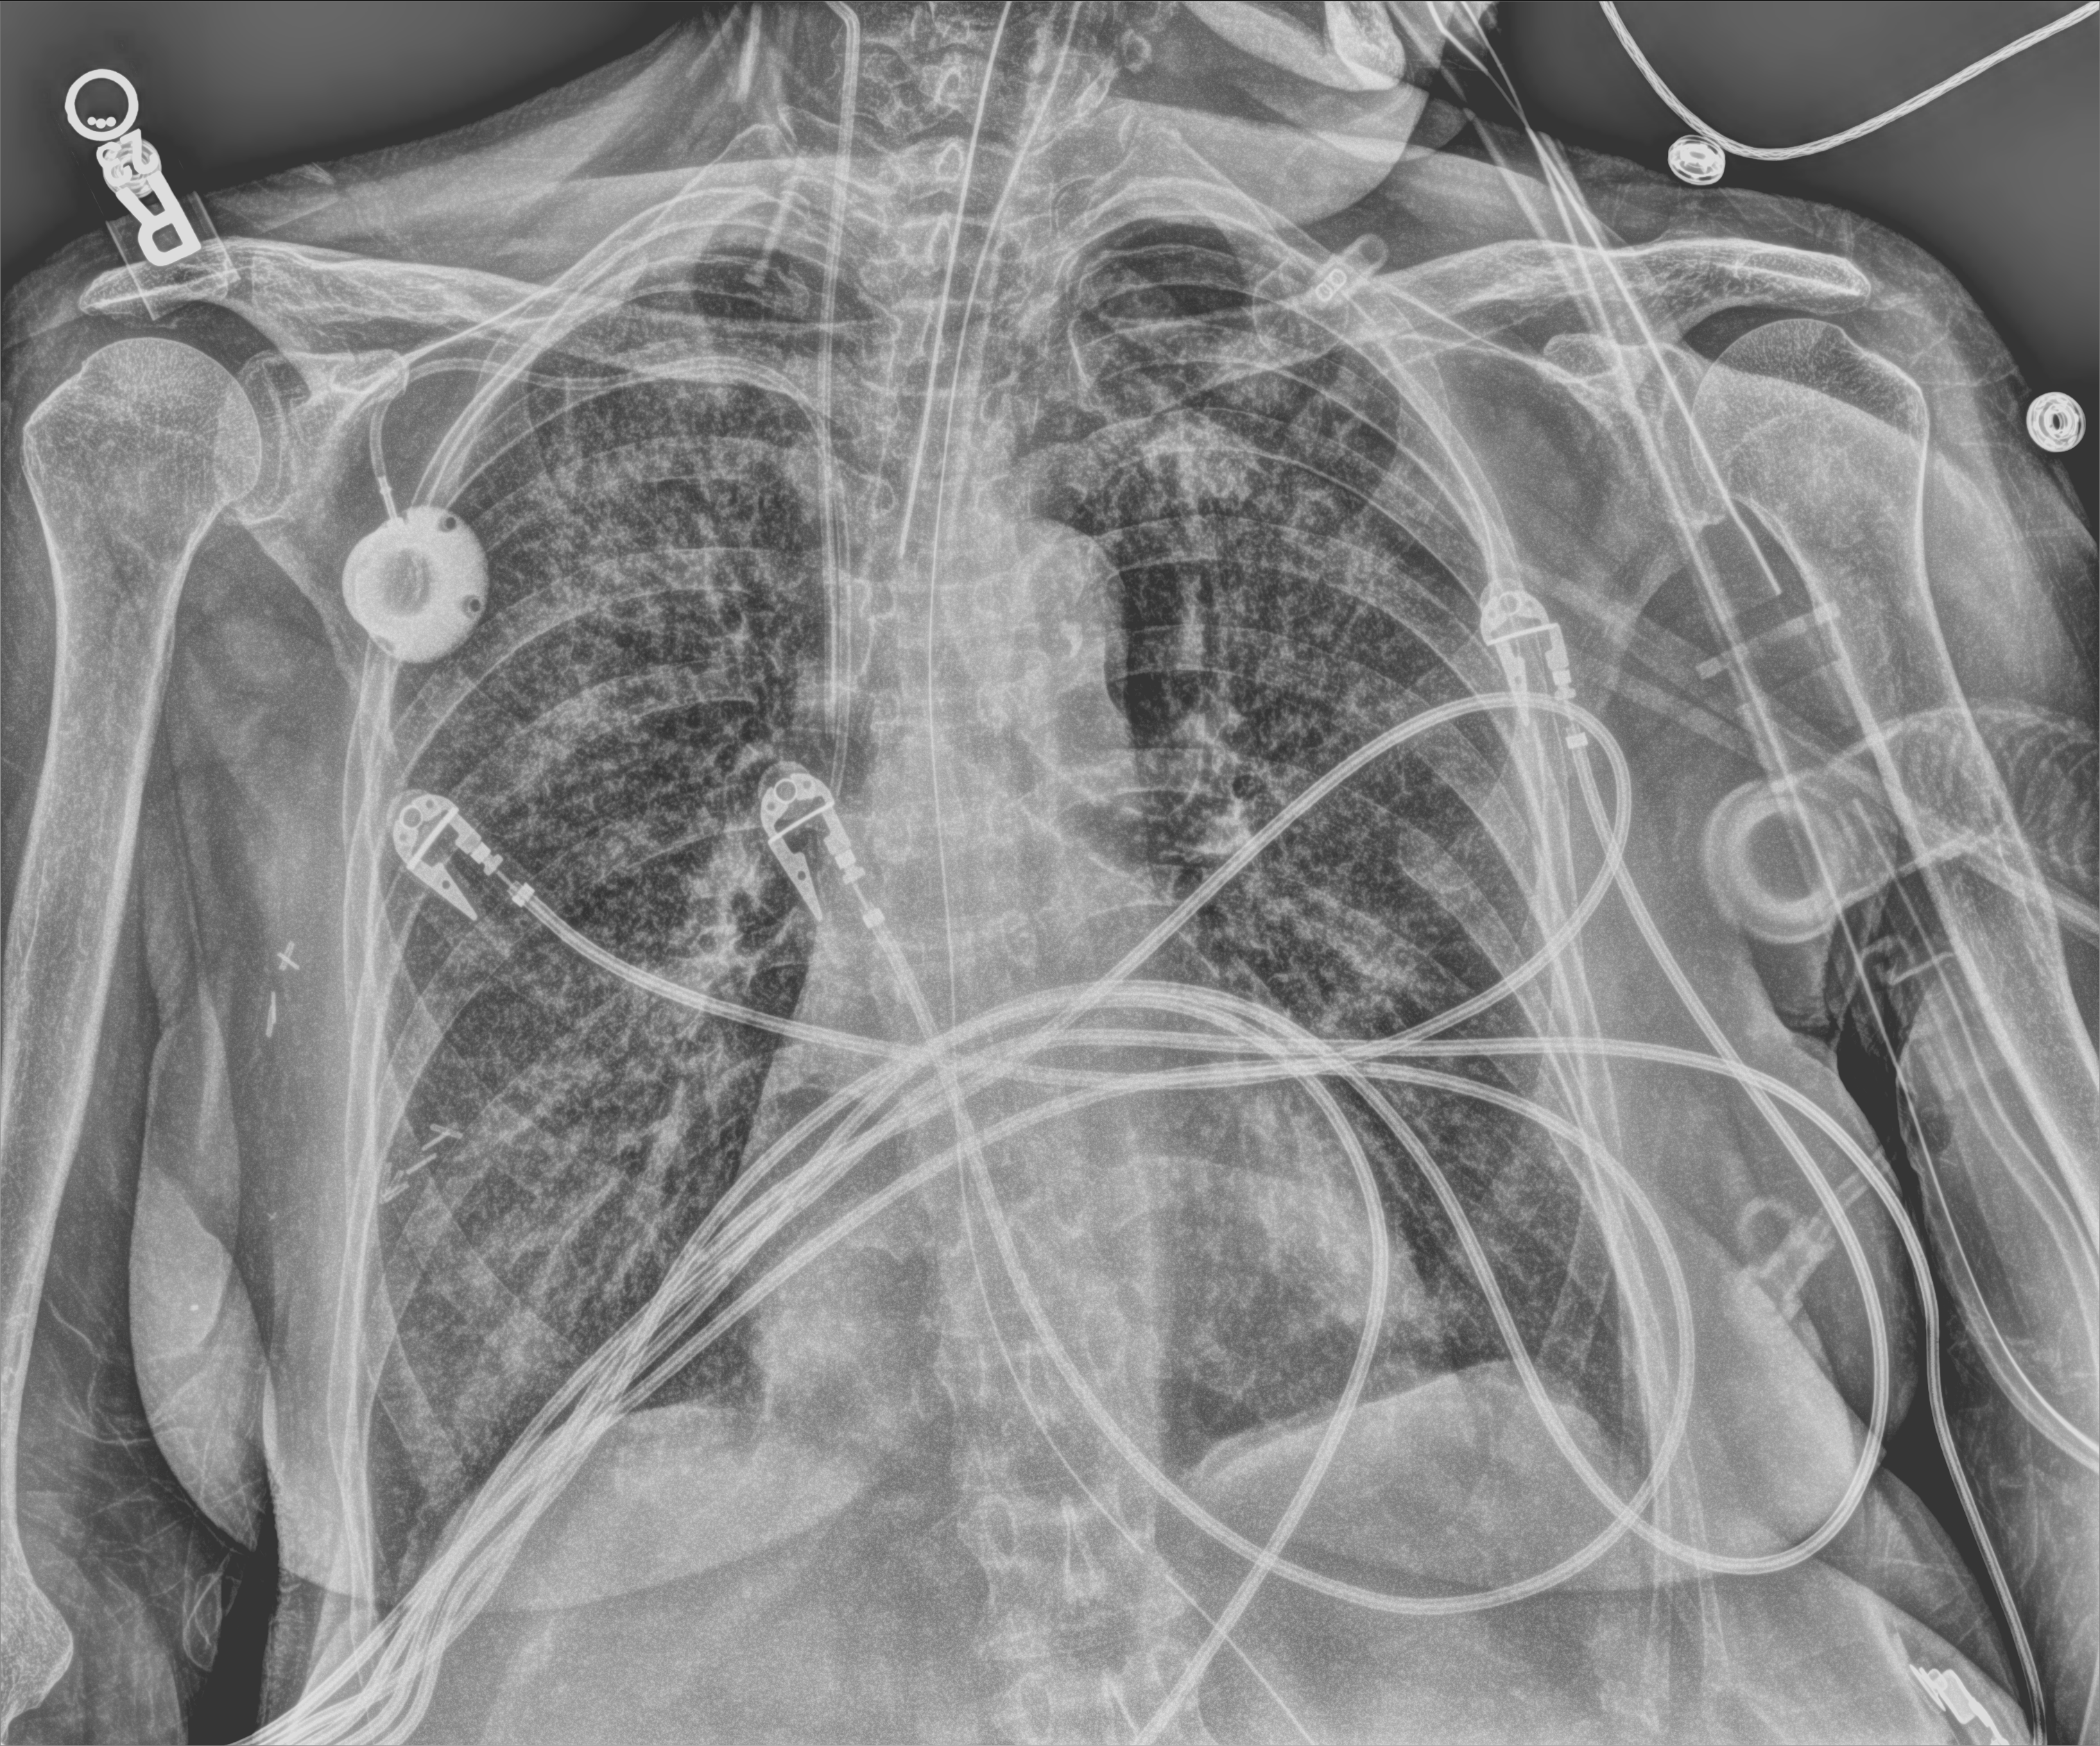
Bedside chest radiograph (computed radiography). Patient hospitalised with COVID-19; female, aged 60–74 years.
Admission-level facts for this patient (not findings on this image; timing relative to this image not recorded):
- mechanically ventilated during this hospital stay: yes
- admitted to intensive care during this hospital stay: yes